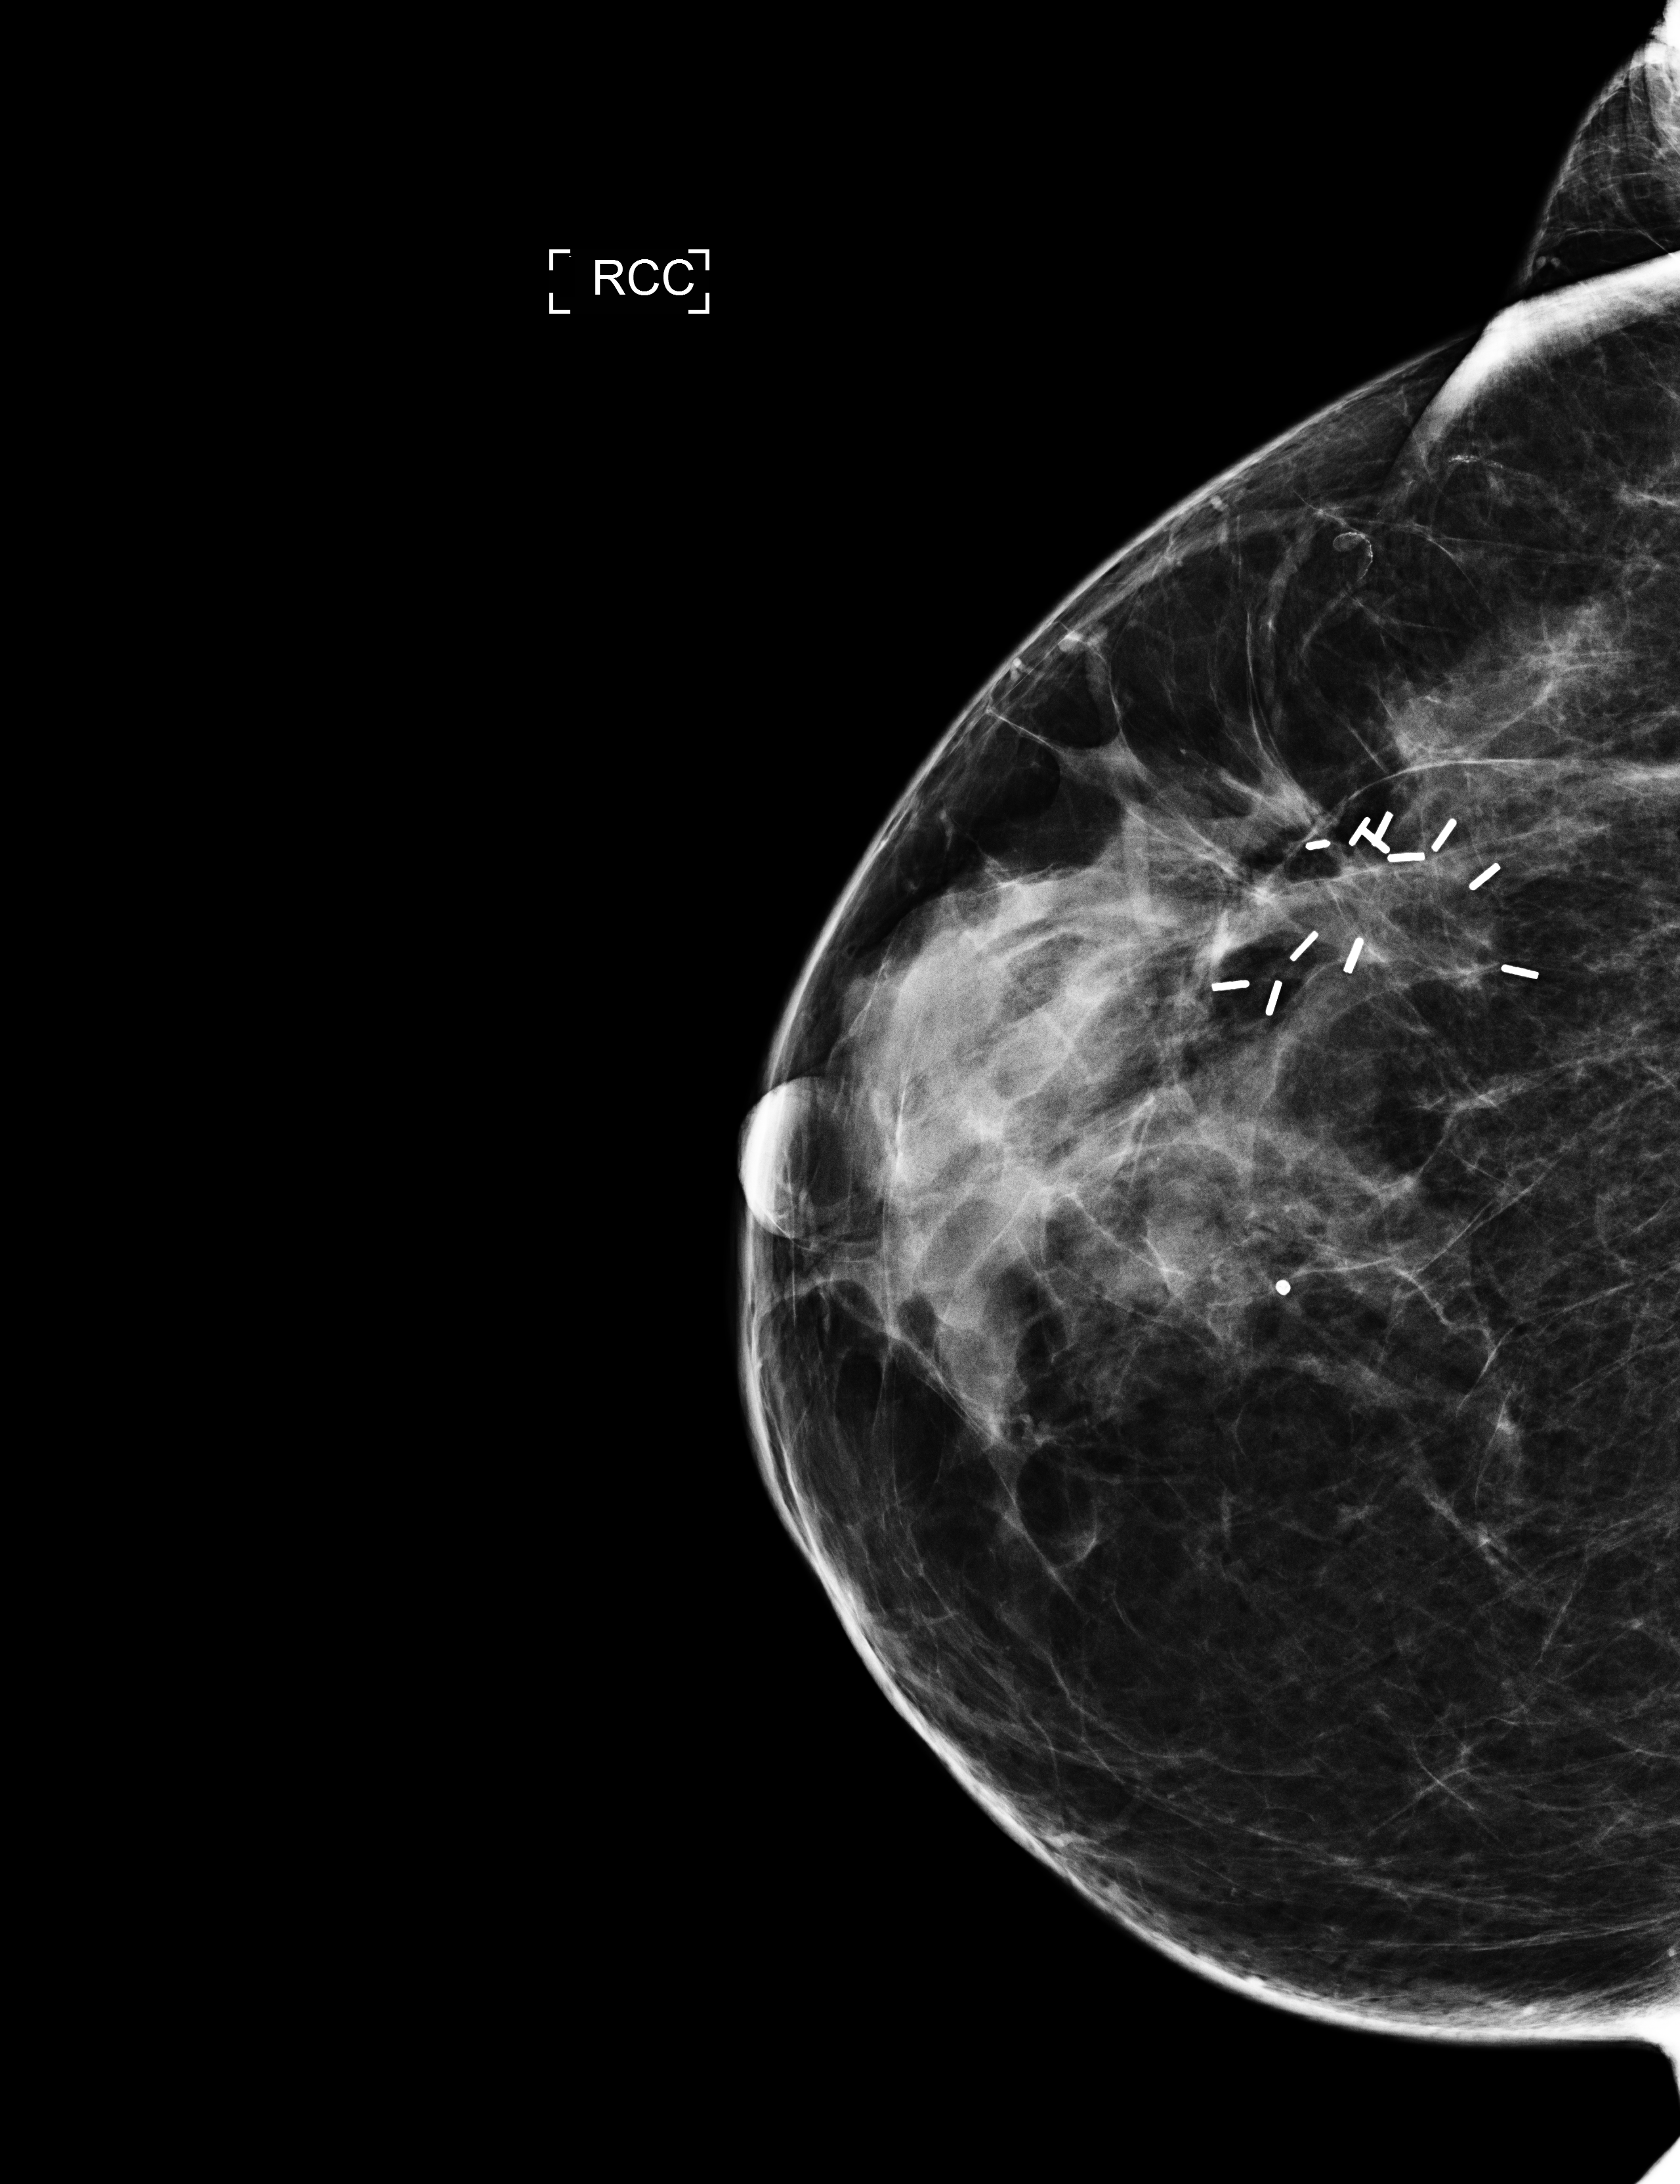
Digital mammogram (FFDM), right breast, craniocaudal (CC) view, screening examination. Female patient, age 48 years.
- breast density at the screening exam (both breasts): heterogeneously dense (BI-RADS density category c)
- final BI-RADS category for the screening round (tomosynthesis exam, both breasts): category 1
- recall: no recall after this screen